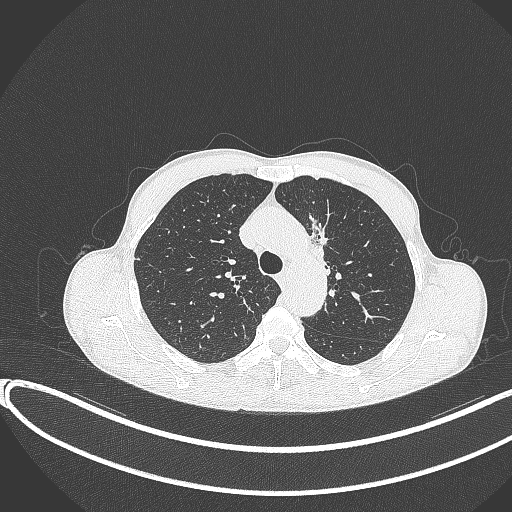
Chest CT, one axial slice; position 274 of 374 along the scan axis; reconstruction kernel B70f; 120 kVp; lung window (W 1500 / L -600 HU); 1 mm slice thickness; 512 × 512 image matrix, field of view 400 × 400 mm. Patient: male, 58 years. Case-level facts recorded for this patient, not image findings: clinical TNM (as recorded): T1c N1 M0.
Structures marked on this image (rectangle marked by the reading radiologist):
- lung tumour (recorded histology: adenocarcinoma): bounding box <301,208,336,268> (left, top, right, bottom; pixels)